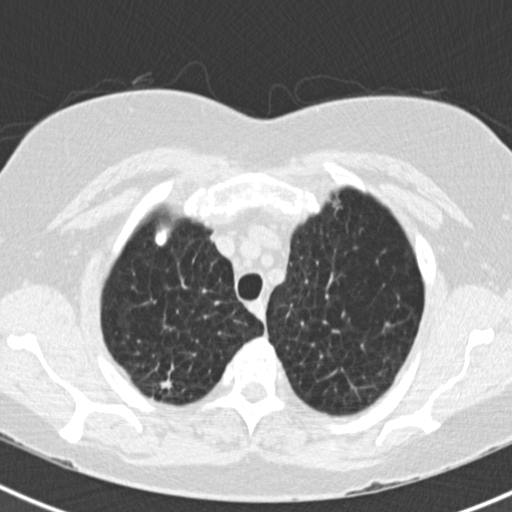
Low-dose screening chest CT, one axial slice; position 145 of 180 along the scan axis; 120 kVp; lung window (W 1500 / L -600 HU); 2 mm slice thickness; 512 × 512 image matrix, field of view 310 × 310 mm.
Structures marked on this image (manually delineated by an expert):
- lesion 1 (tumor, upper lobe of right lung): bounding box (x1, y1, x2, y2) in pixels: (160, 378, 172, 389)